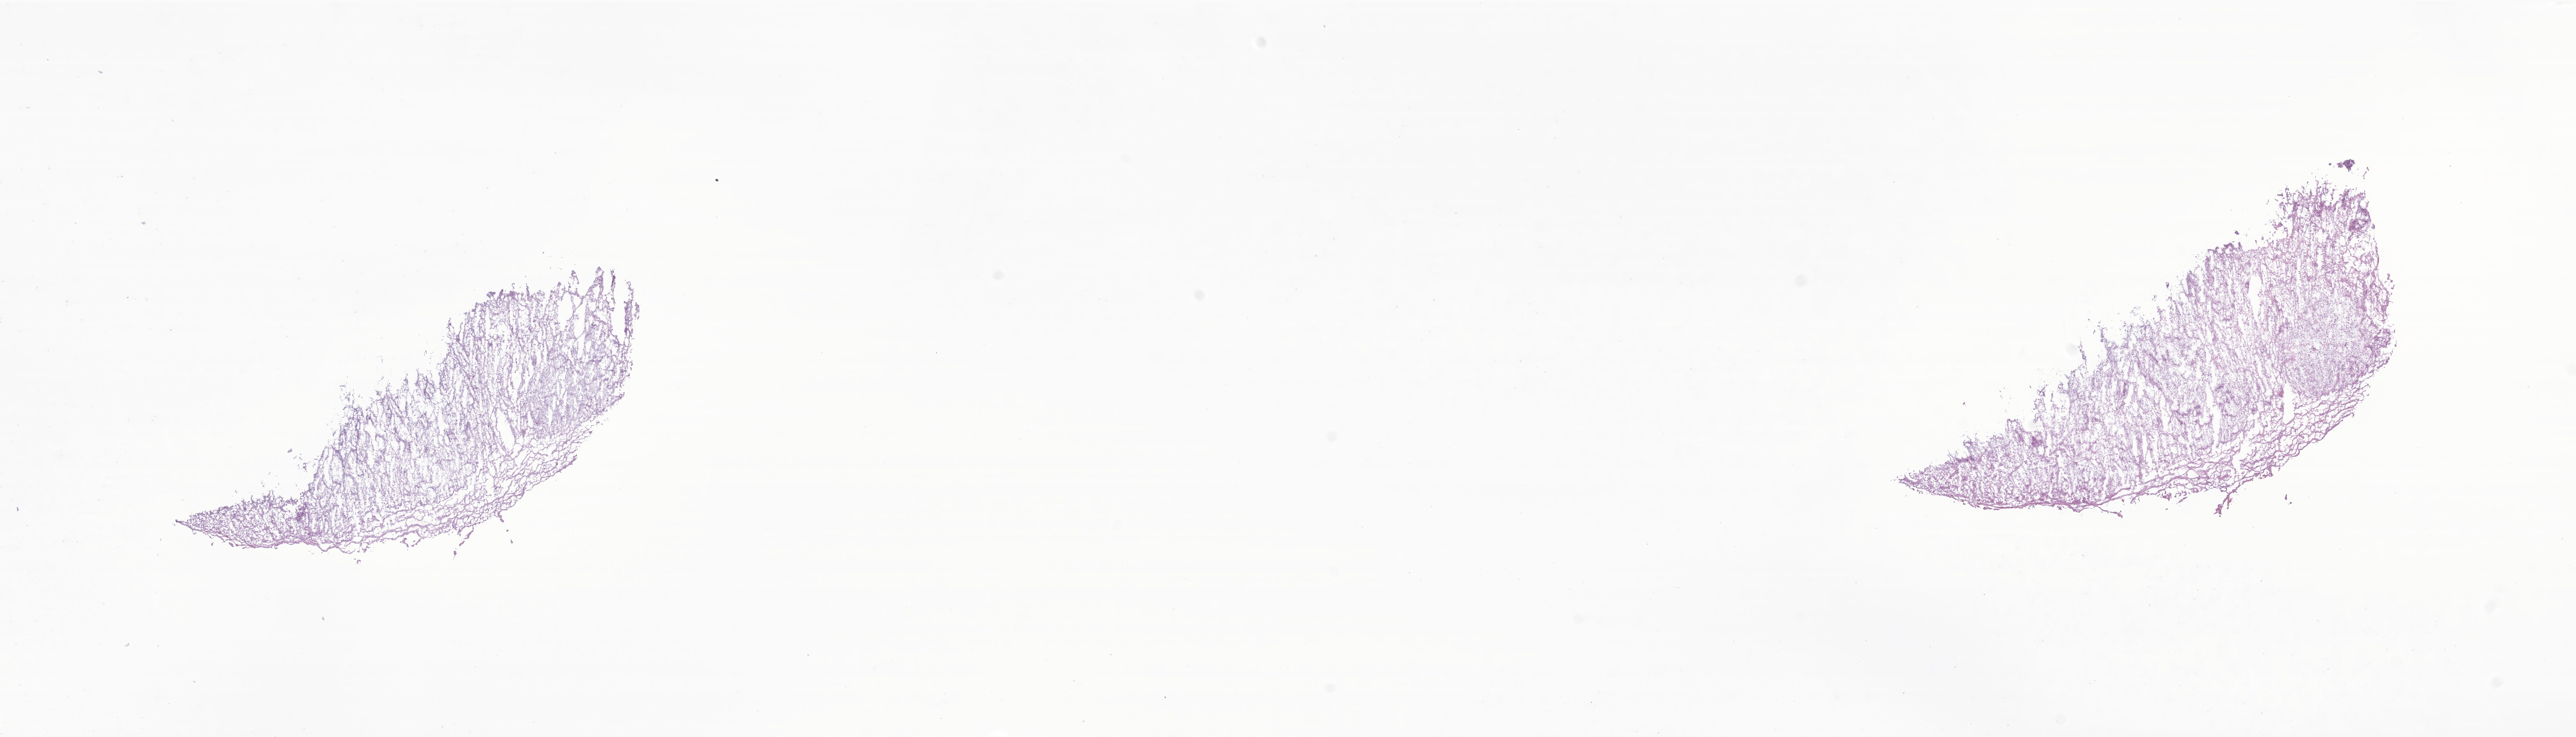
Hematoxylin and eosin (H&E) whole-slide image of tumor tissue from the brain, low-resolution overview of the scanned area, about 26.3 x 7.5 mm; frozen section (OCT-embedded). Male patient, age 147 months (12 years 3 months).
Diagnosis: Mesenchymal chondrosarcoma.